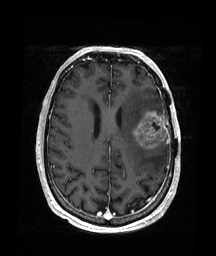
Brain MRI from a brain-tumour surgery series, one axial slice. Slice 69 of 176 in the series (ordered by position). T1-weighted post-contrast. 1 mm slice thickness. 216 × 256 image matrix. Case-level facts recorded for this patient, not image findings: histopathology: Glioblastoma; WHO grade: 4; IDH mutation: no; tumour location: Left Frontal.
Structures marked on this image (manually delineated by an expert):
- tumour: bounding box (x1, y1, x2, y2) in pixels: (132, 110, 168, 150)